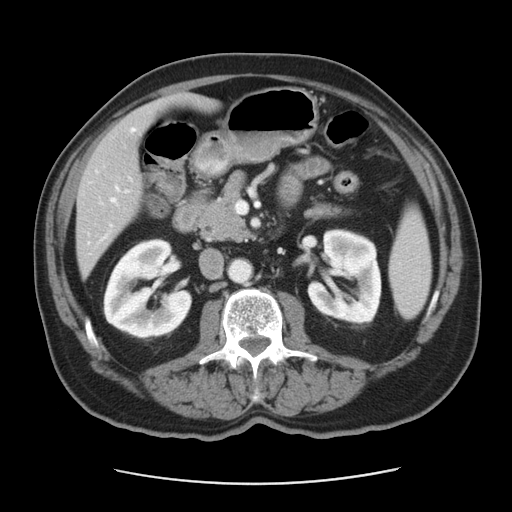
Contrast-enhanced abdominal CT, one axial slice. Slice 18 of 42 in the series (ordered by position). 120 kVp. Intravenous contrast given. Soft-tissue window (W 400 / L 40 HU). 5 mm slice thickness. 512 × 512 image matrix, field of view 370 × 370 mm. Male patient, age 73 years. From the clinical record (not read from this slice): diagnosis: colorectal cancer liver metastases, imaged before liver resection; multiple liver metastases: yes; largest metastasis: 0.5 cm; chemotherapy before resection: yes.
Annotated regions visible in this slice (expert manual segmentation):
- hepatic veins: bounding box <88,129,135,243> (left, top, right, bottom; pixels)
- liver: <77,98,213,274>
- planned liver remnant (the part of the liver to remain after resection): <110,98,214,157>